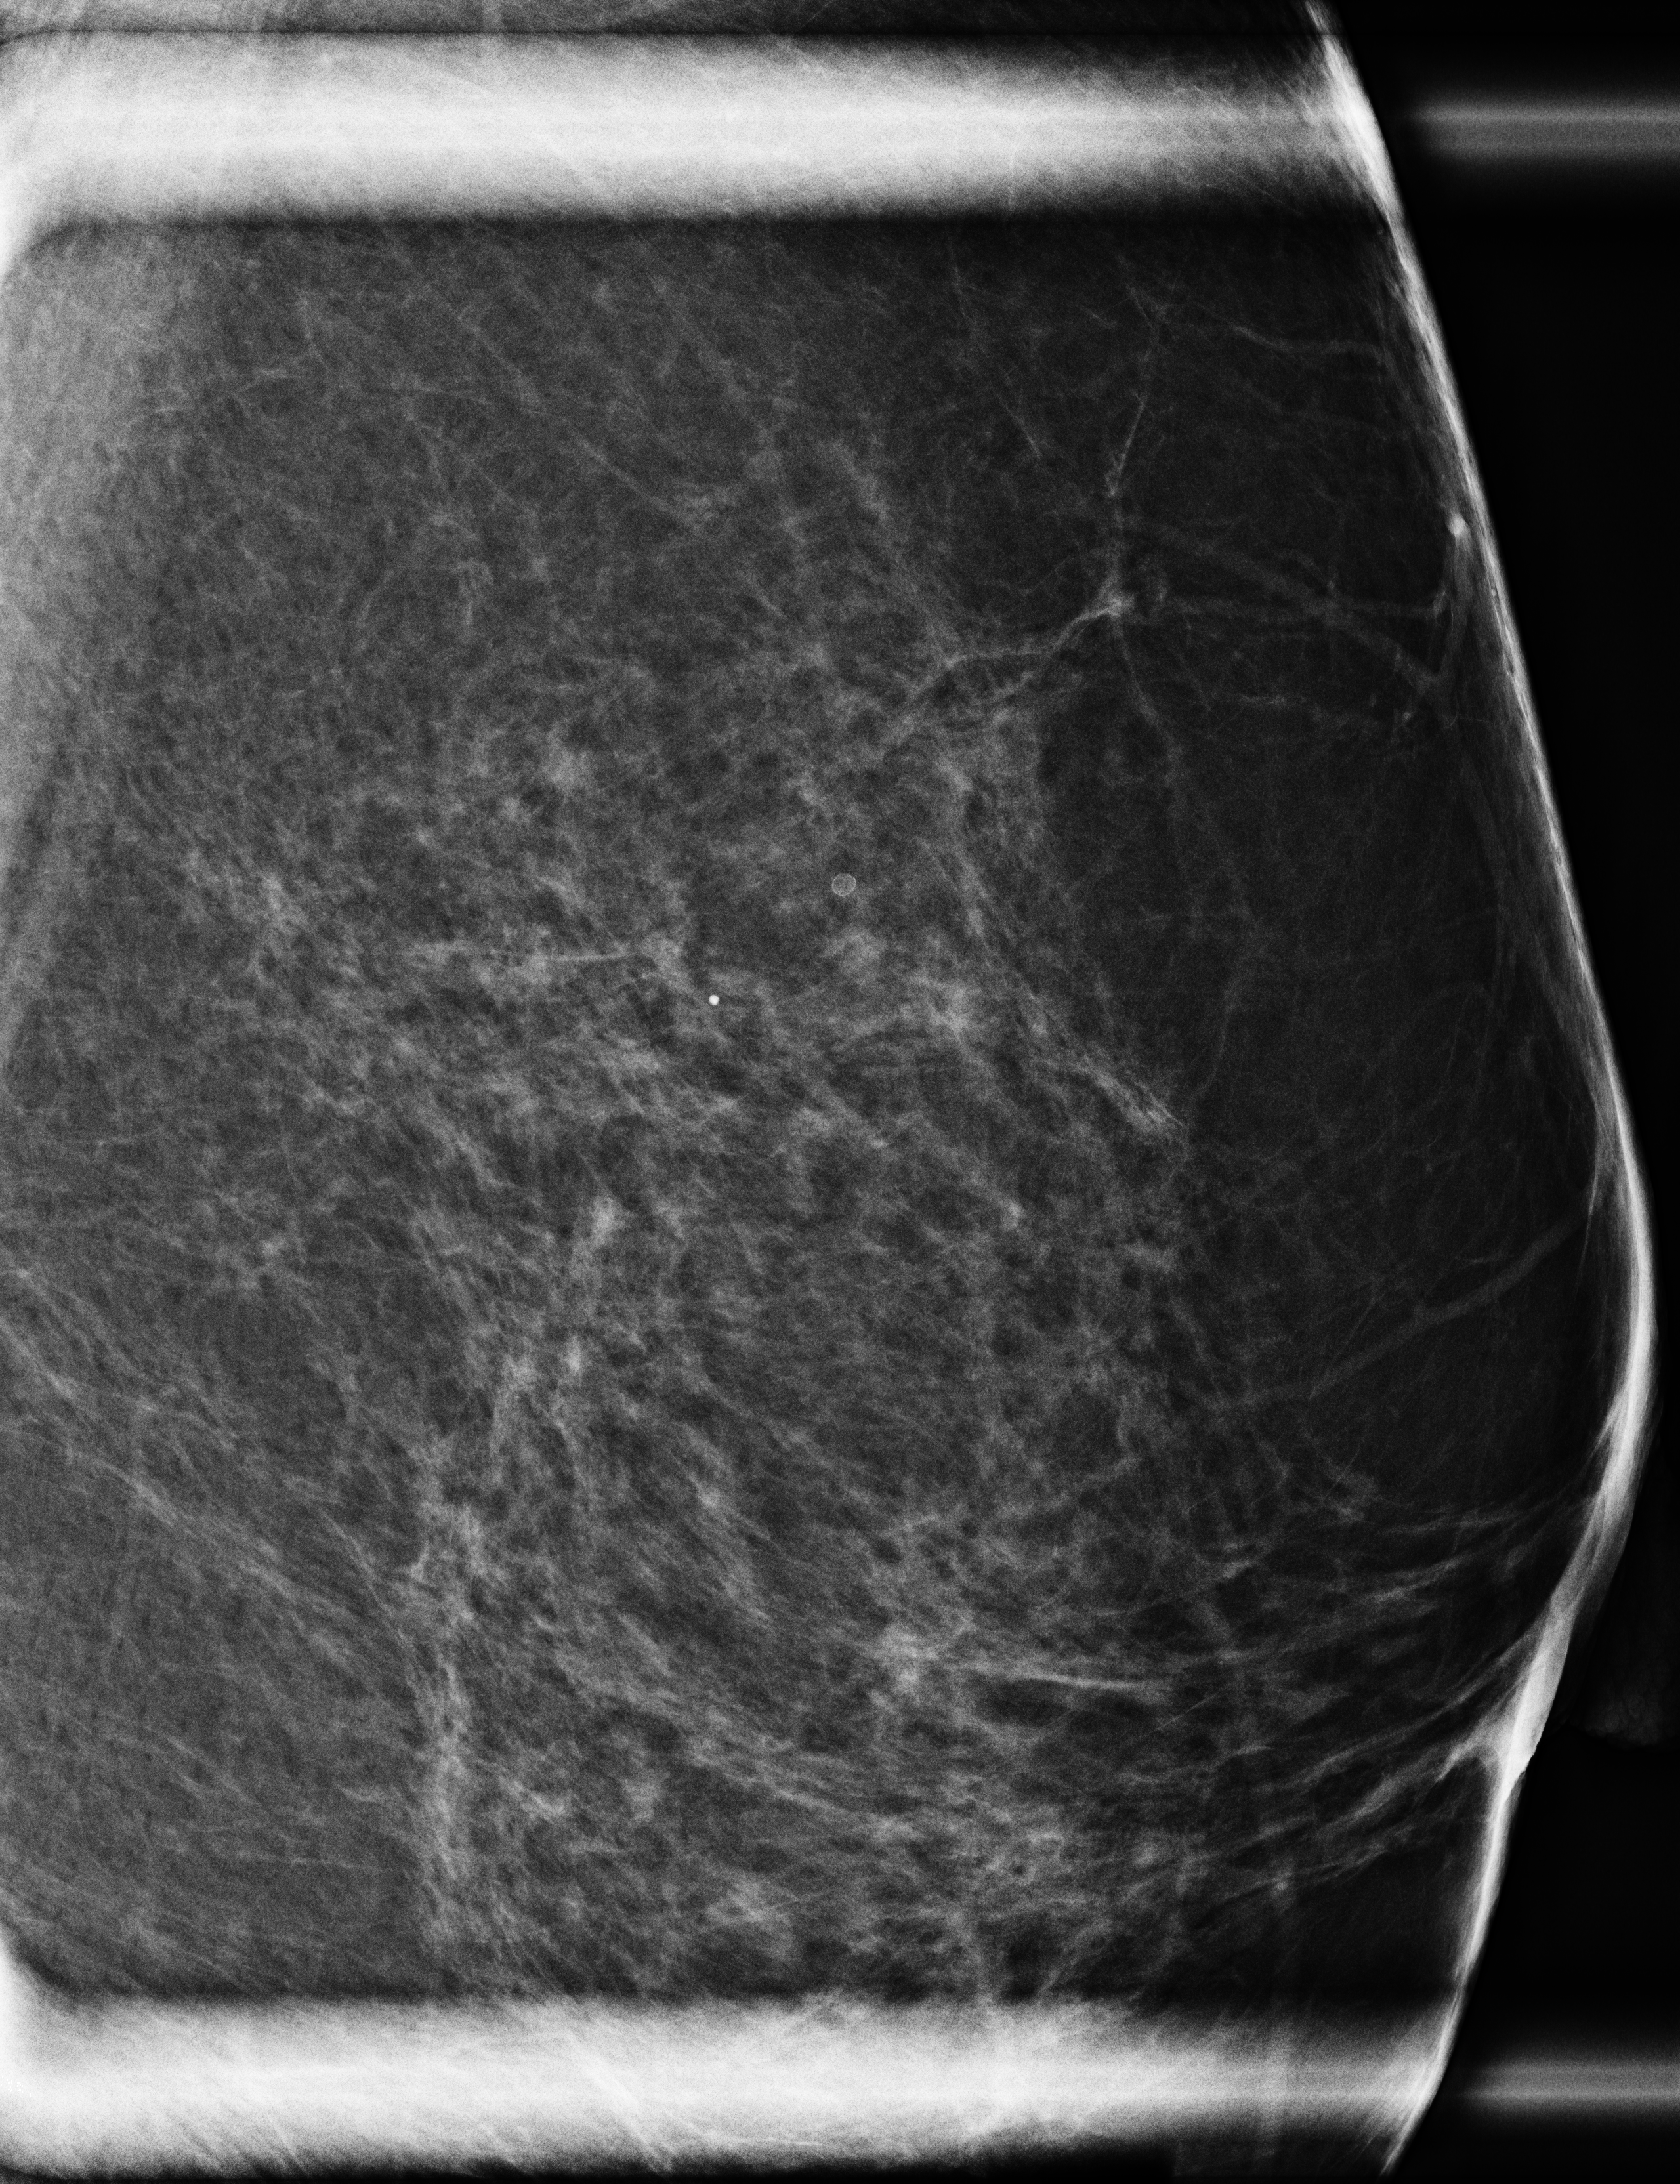
Full-field digital mammogram (FFDM); left breast; ML view (magnification); additional (diagnostic) view; system: Selenia Dimensions. Female patient, age 74 years.
Breast density at the screening exam (both breasts): heterogeneously dense (BI-RADS density category c). Final BI-RADS assessment for this screening round (tomosynthesis exam, both breasts): category 4. Recall: recalled for additional imaging after this screen.